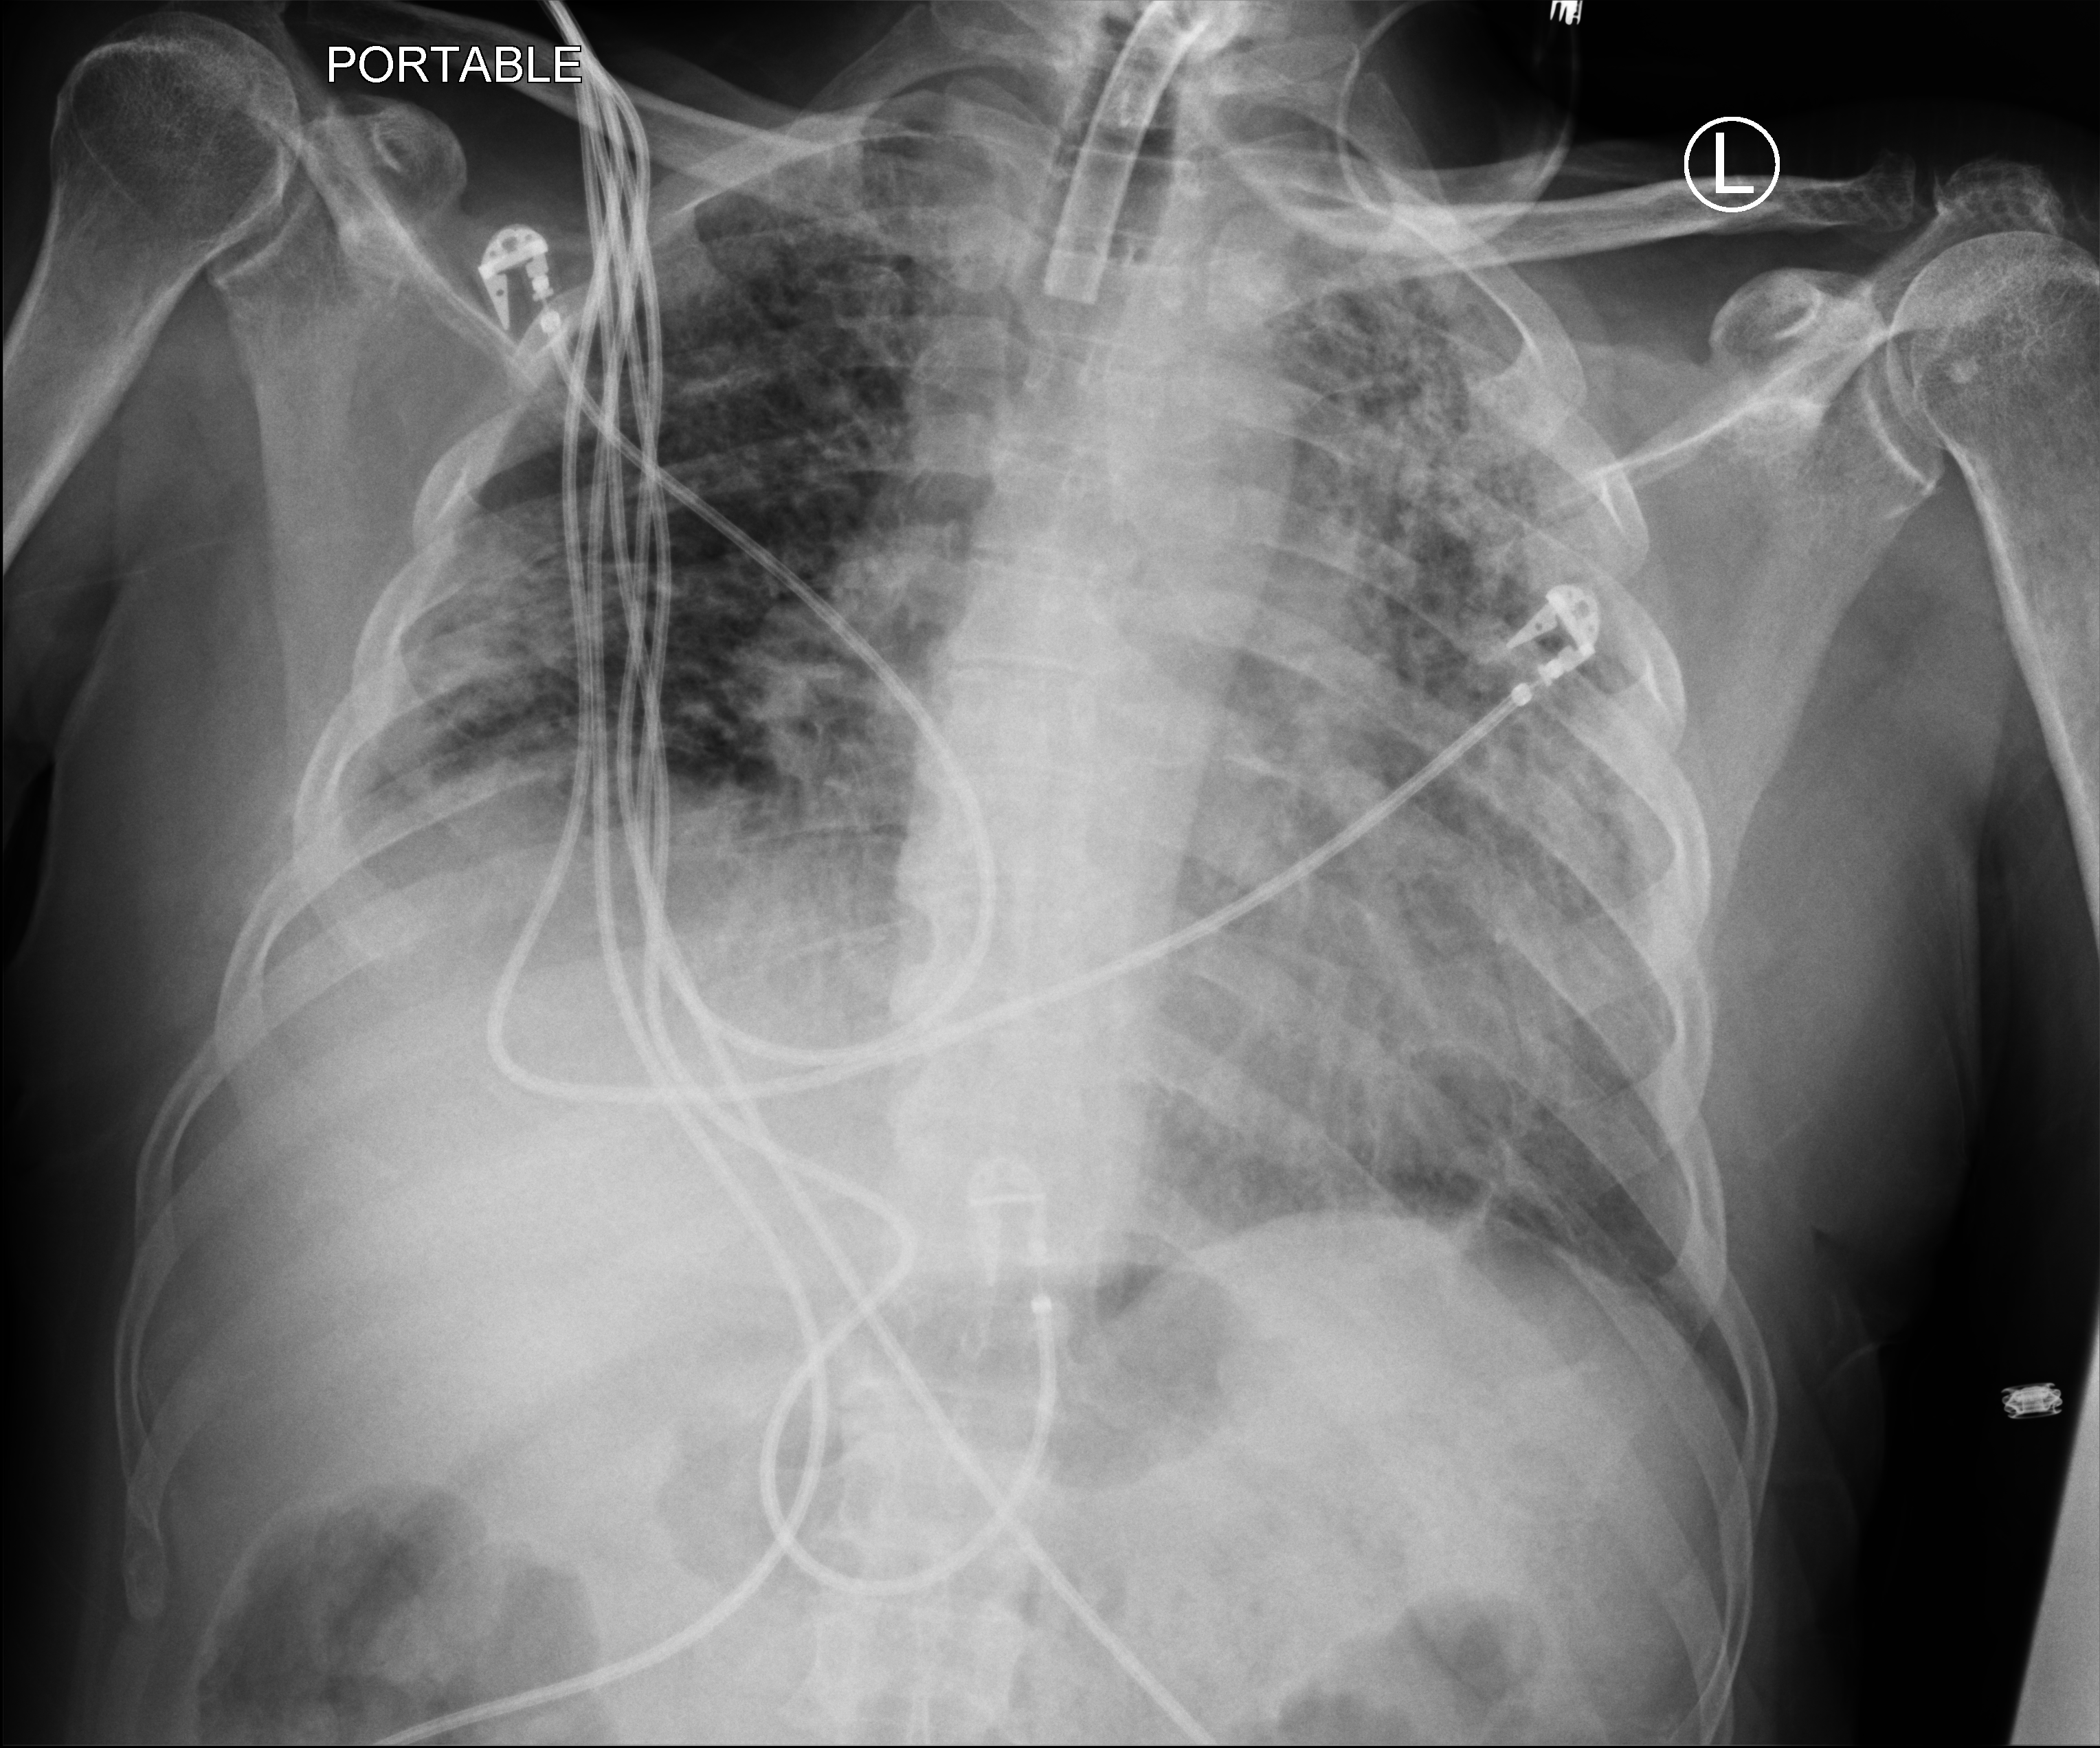
Chest X-ray (portable), anteroposterior (AP) projection. Patient hospitalised with COVID-19; male, aged 18–59 years.
From the hospital-stay record, not from the radiograph (when in the stay this image was taken is not recorded):
- admitted to intensive care during this hospital stay: yes
- mechanically ventilated during this hospital stay: yes
- length of hospital stay: 83 days